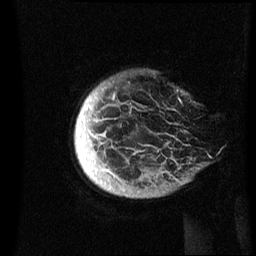
Breast MRI (dynamic contrast-enhanced), one sagittal slice; slice 1 of 60 in the series (ordered by position); dynamic contrast-enhanced series, image 2 of 3 at this slice position (ordered by acquisition); 1.5 T; TE 4.2 ms, TR 8.4 ms; 2.4 mm slice thickness; 256 × 256 image matrix, field of view 230 × 230 mm. Female patient, age 48 years.
Annotated regions visible in this slice (semi-automatically segmented with operator editing):
- analysis volume of interest (the breast-tissue region the enhancement analysis was run in; not a lesion): bounding box [x1, y1, x2, y2] px = [75, 82, 201, 198]
- tumour enhancement mask (voxels above the 70 % enhancement threshold inside the analysis volume of interest): [76, 95, 115, 177]